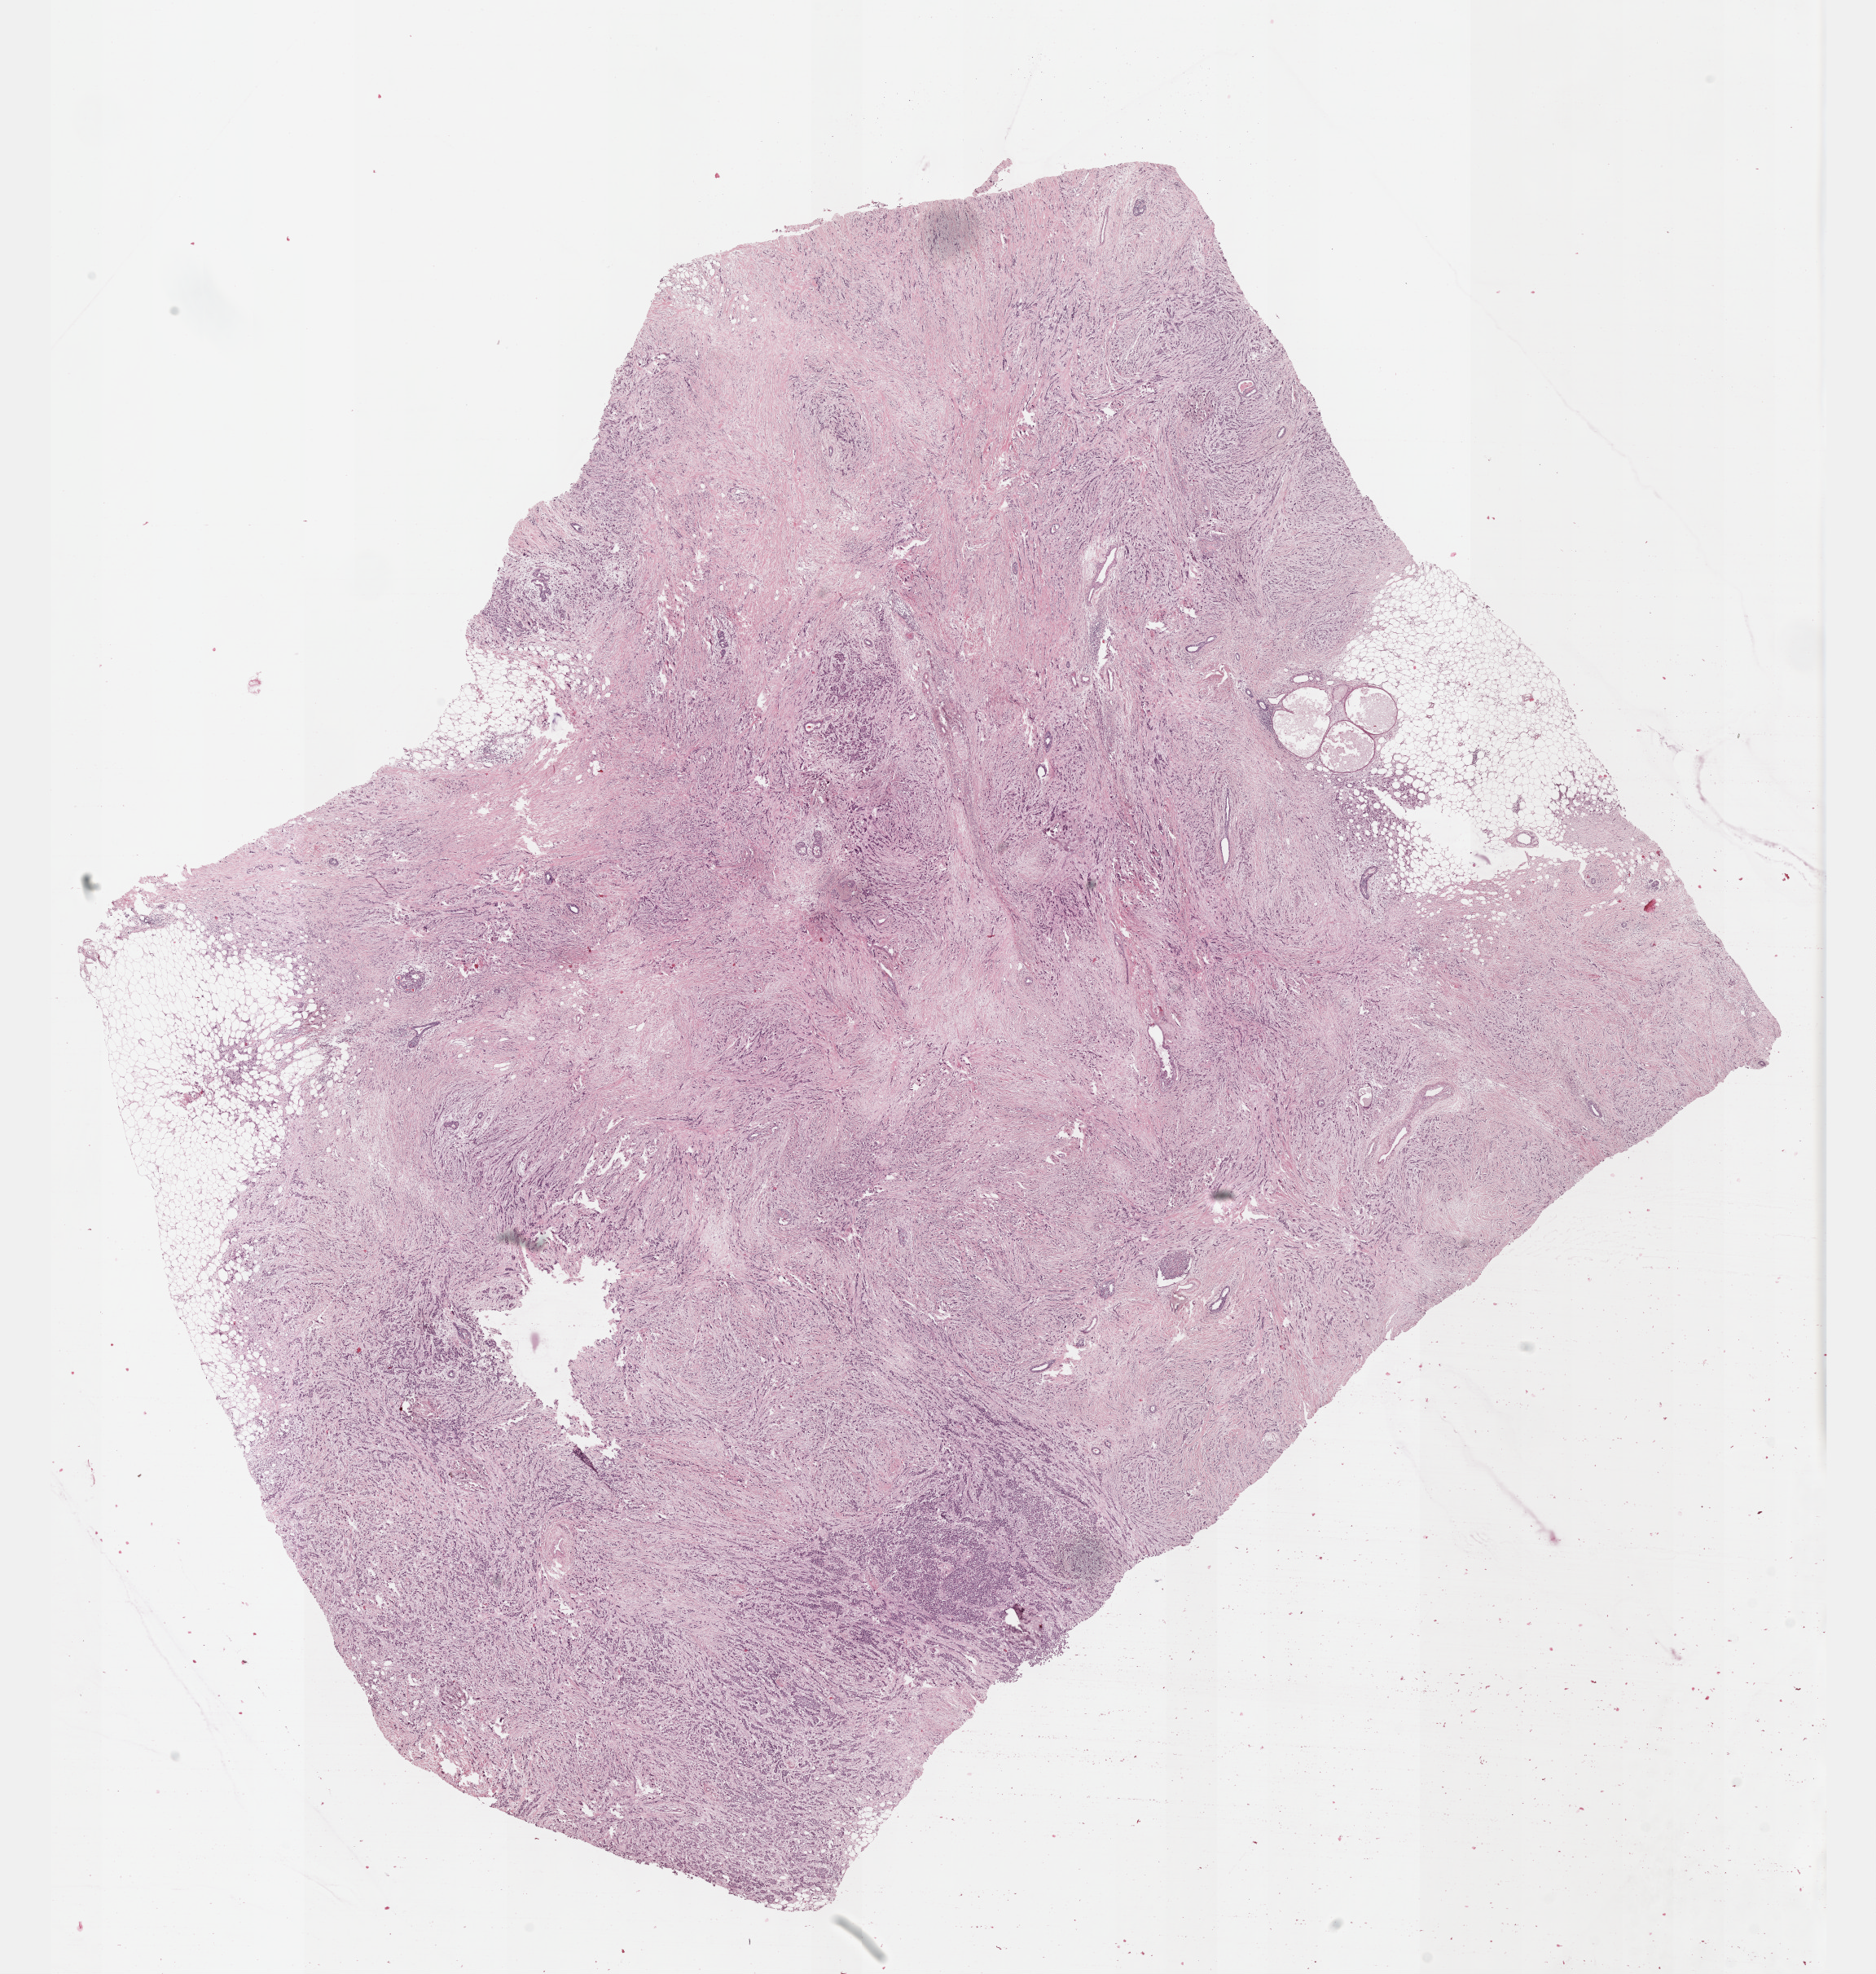
Digitized H&E tissue section (whole slide), a low-resolution overview of the entire scanned area, about 18.6 x 19.6 mm (acquisition: 40x scan). FFPE section. Primary tumour sample from the breast. Patient: female, age at initial diagnosis 50 years.
• diagnosis: Lobular carcinoma, NOS
• lymph nodes positive (case pathology): 4 of 14 examined
• laterality: left
• AJCC pathologic stage: IIIA (7th edition)
• TNM: T2 N2a M0